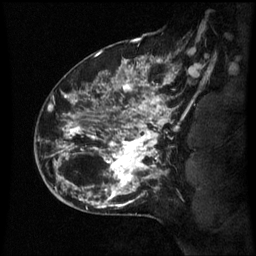
Breast MRI (dynamic contrast-enhanced), one sagittal slice; position 45 of 60 along the scan axis; dynamic contrast-enhanced series, image 2 of 3 at this slice position (ordered by acquisition); 1.5 T; TE 4.2 ms, TR 8.9 ms; 2.1 mm slice thickness; 256 × 256 image matrix, field of view 200 × 200 mm. Female patient, age 42 years. Case-level facts recorded for this patient, not image findings: setting: breast cancer imaged before/during neoadjuvant chemotherapy; receptor status: HER2-positive.
Outlined on this slice (semi-automatically segmented with operator editing):
- analysis volume of interest (the breast-tissue region the enhancement analysis was run in; not a lesion): box from (x=66, y=82) to (x=173, y=193) px
- tumour enhancement mask (voxels above the 70 % enhancement threshold inside the analysis volume of interest): (x=66, y=82)–(x=173, y=193)